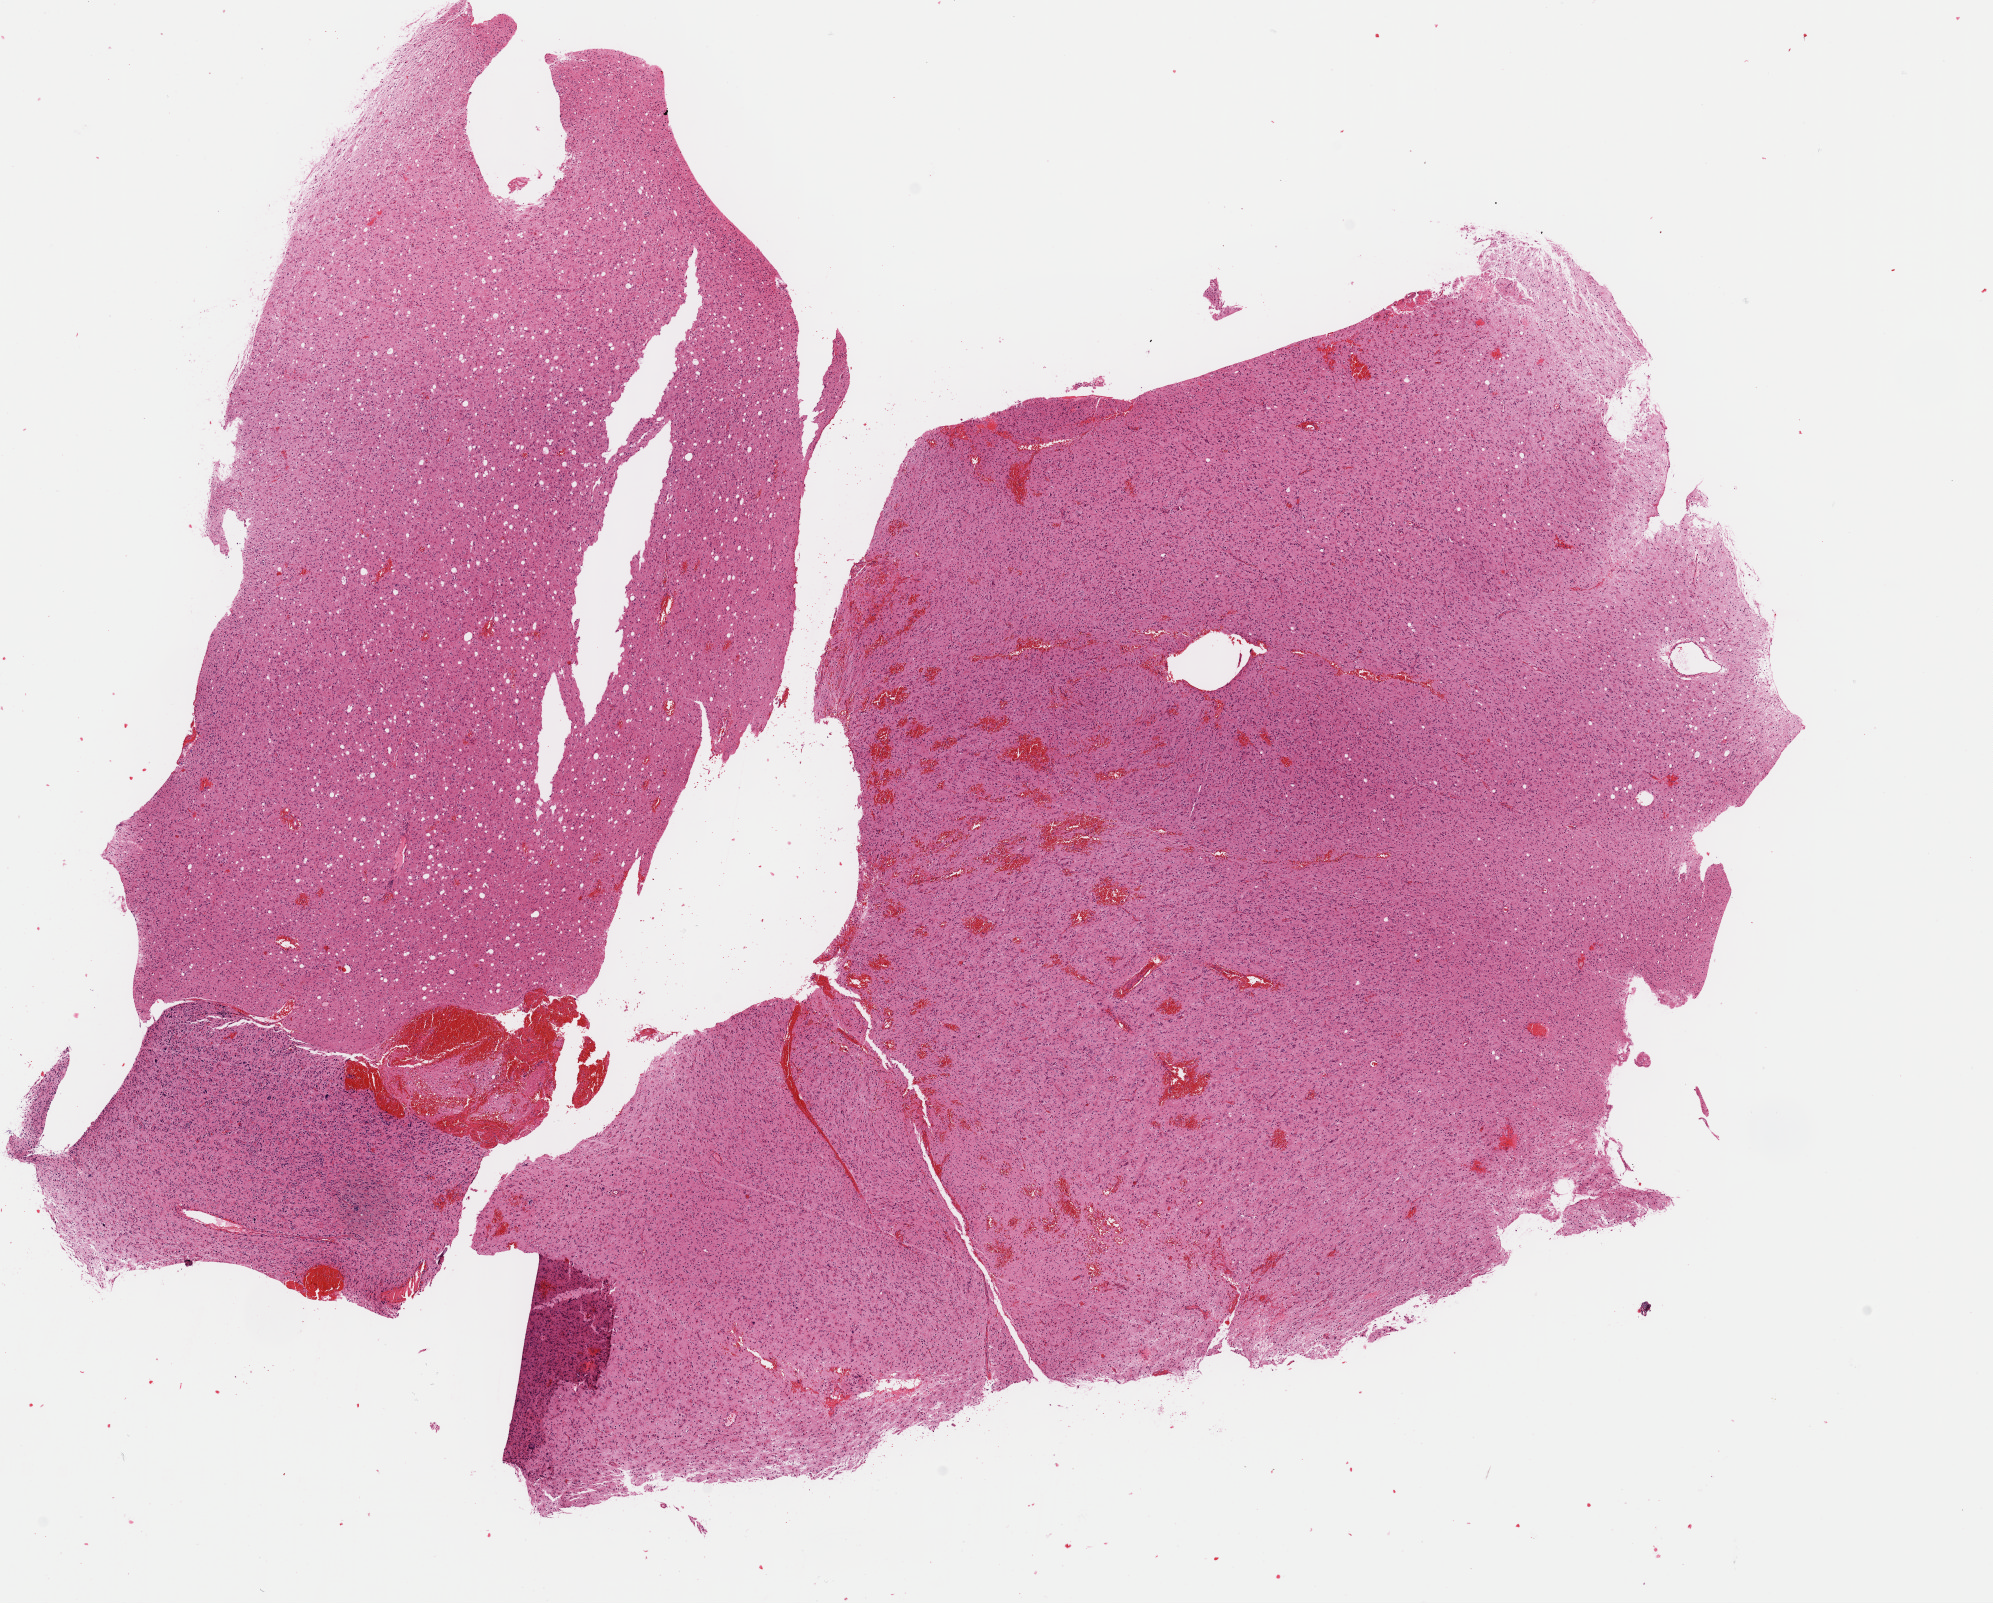
H&E whole-slide image — whole scanned area (about 15.7 x 12.7 mm) shown as a low-resolution overview, formalin-fixed paraffin-embedded (FFPE) diagnostic section, primary tumour sample from the brain. Male patient; age at initial diagnosis 63 years. Histologic grade: G3 (poorly differentiated).
Pathologic diagnosis: Mixed glioma (frontal lobe).